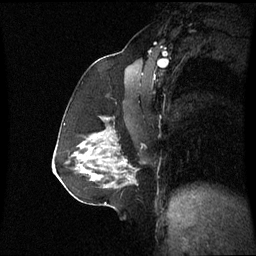
Breast MRI (dynamic contrast-enhanced), one sagittal slice. Position 33 of 60 along the scan axis. Dynamic contrast-enhanced series, image 2 of 3 at this slice position (ordered by acquisition). 1.5 T. TE 4.2 ms, TR 8.9 ms. 2.4 mm slice thickness. 256 × 256 image matrix, field of view 230 × 230 mm. Patient: female, 59 years. Case-level facts recorded for this patient, not image findings: setting: breast cancer imaged before/during neoadjuvant chemotherapy; receptor status: triple-negative.
Annotated regions visible in this slice (semi-automatically segmented with operator editing):
- analysis volume of interest (the breast-tissue region the enhancement analysis was run in; not a lesion): box from (x=86, y=126) to (x=135, y=183) px
- tumour enhancement mask (voxels above the 70 % enhancement threshold inside the analysis volume of interest): (x=121, y=161)–(x=123, y=163)